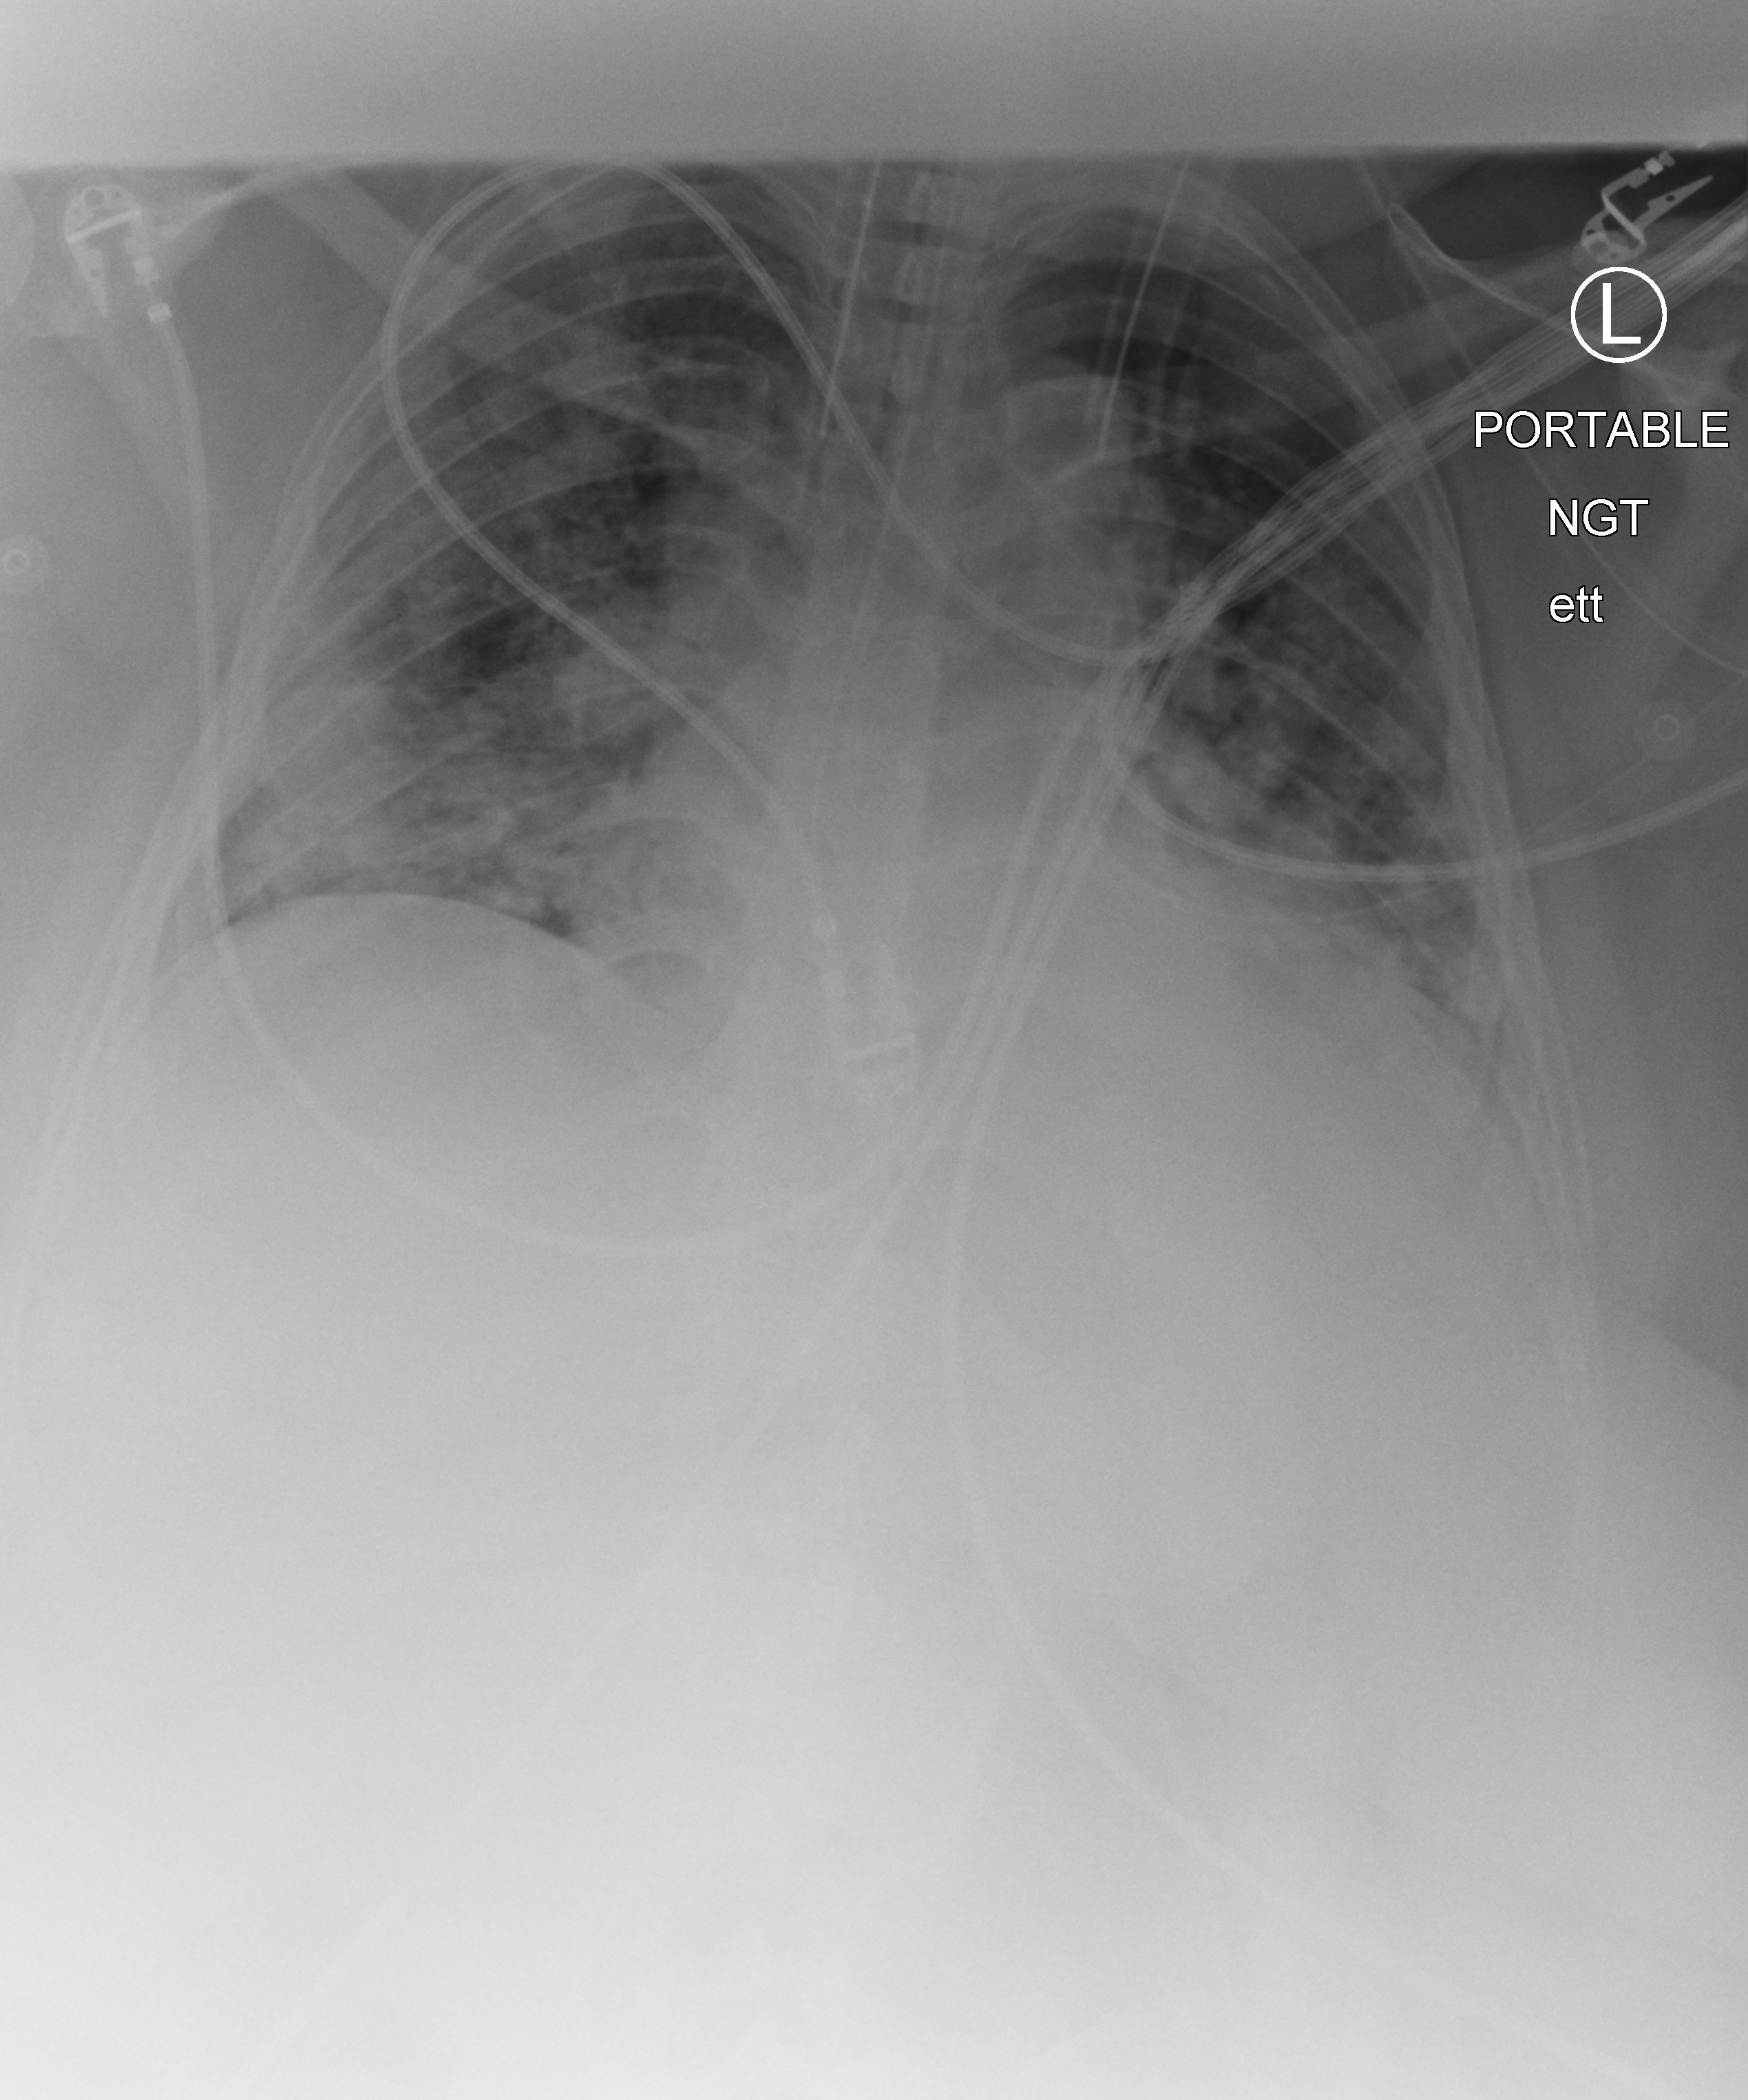
Bedside chest radiograph (computed radiography), anteroposterior (AP) projection. Patient hospitalised with COVID-19; female, aged 18–59 years.
From the hospital-stay record, not from the radiograph (when in the stay this image was taken is not recorded): hypertension (admission record): no; admitted to intensive care during this hospital stay: yes; mechanically ventilated during this hospital stay: yes.